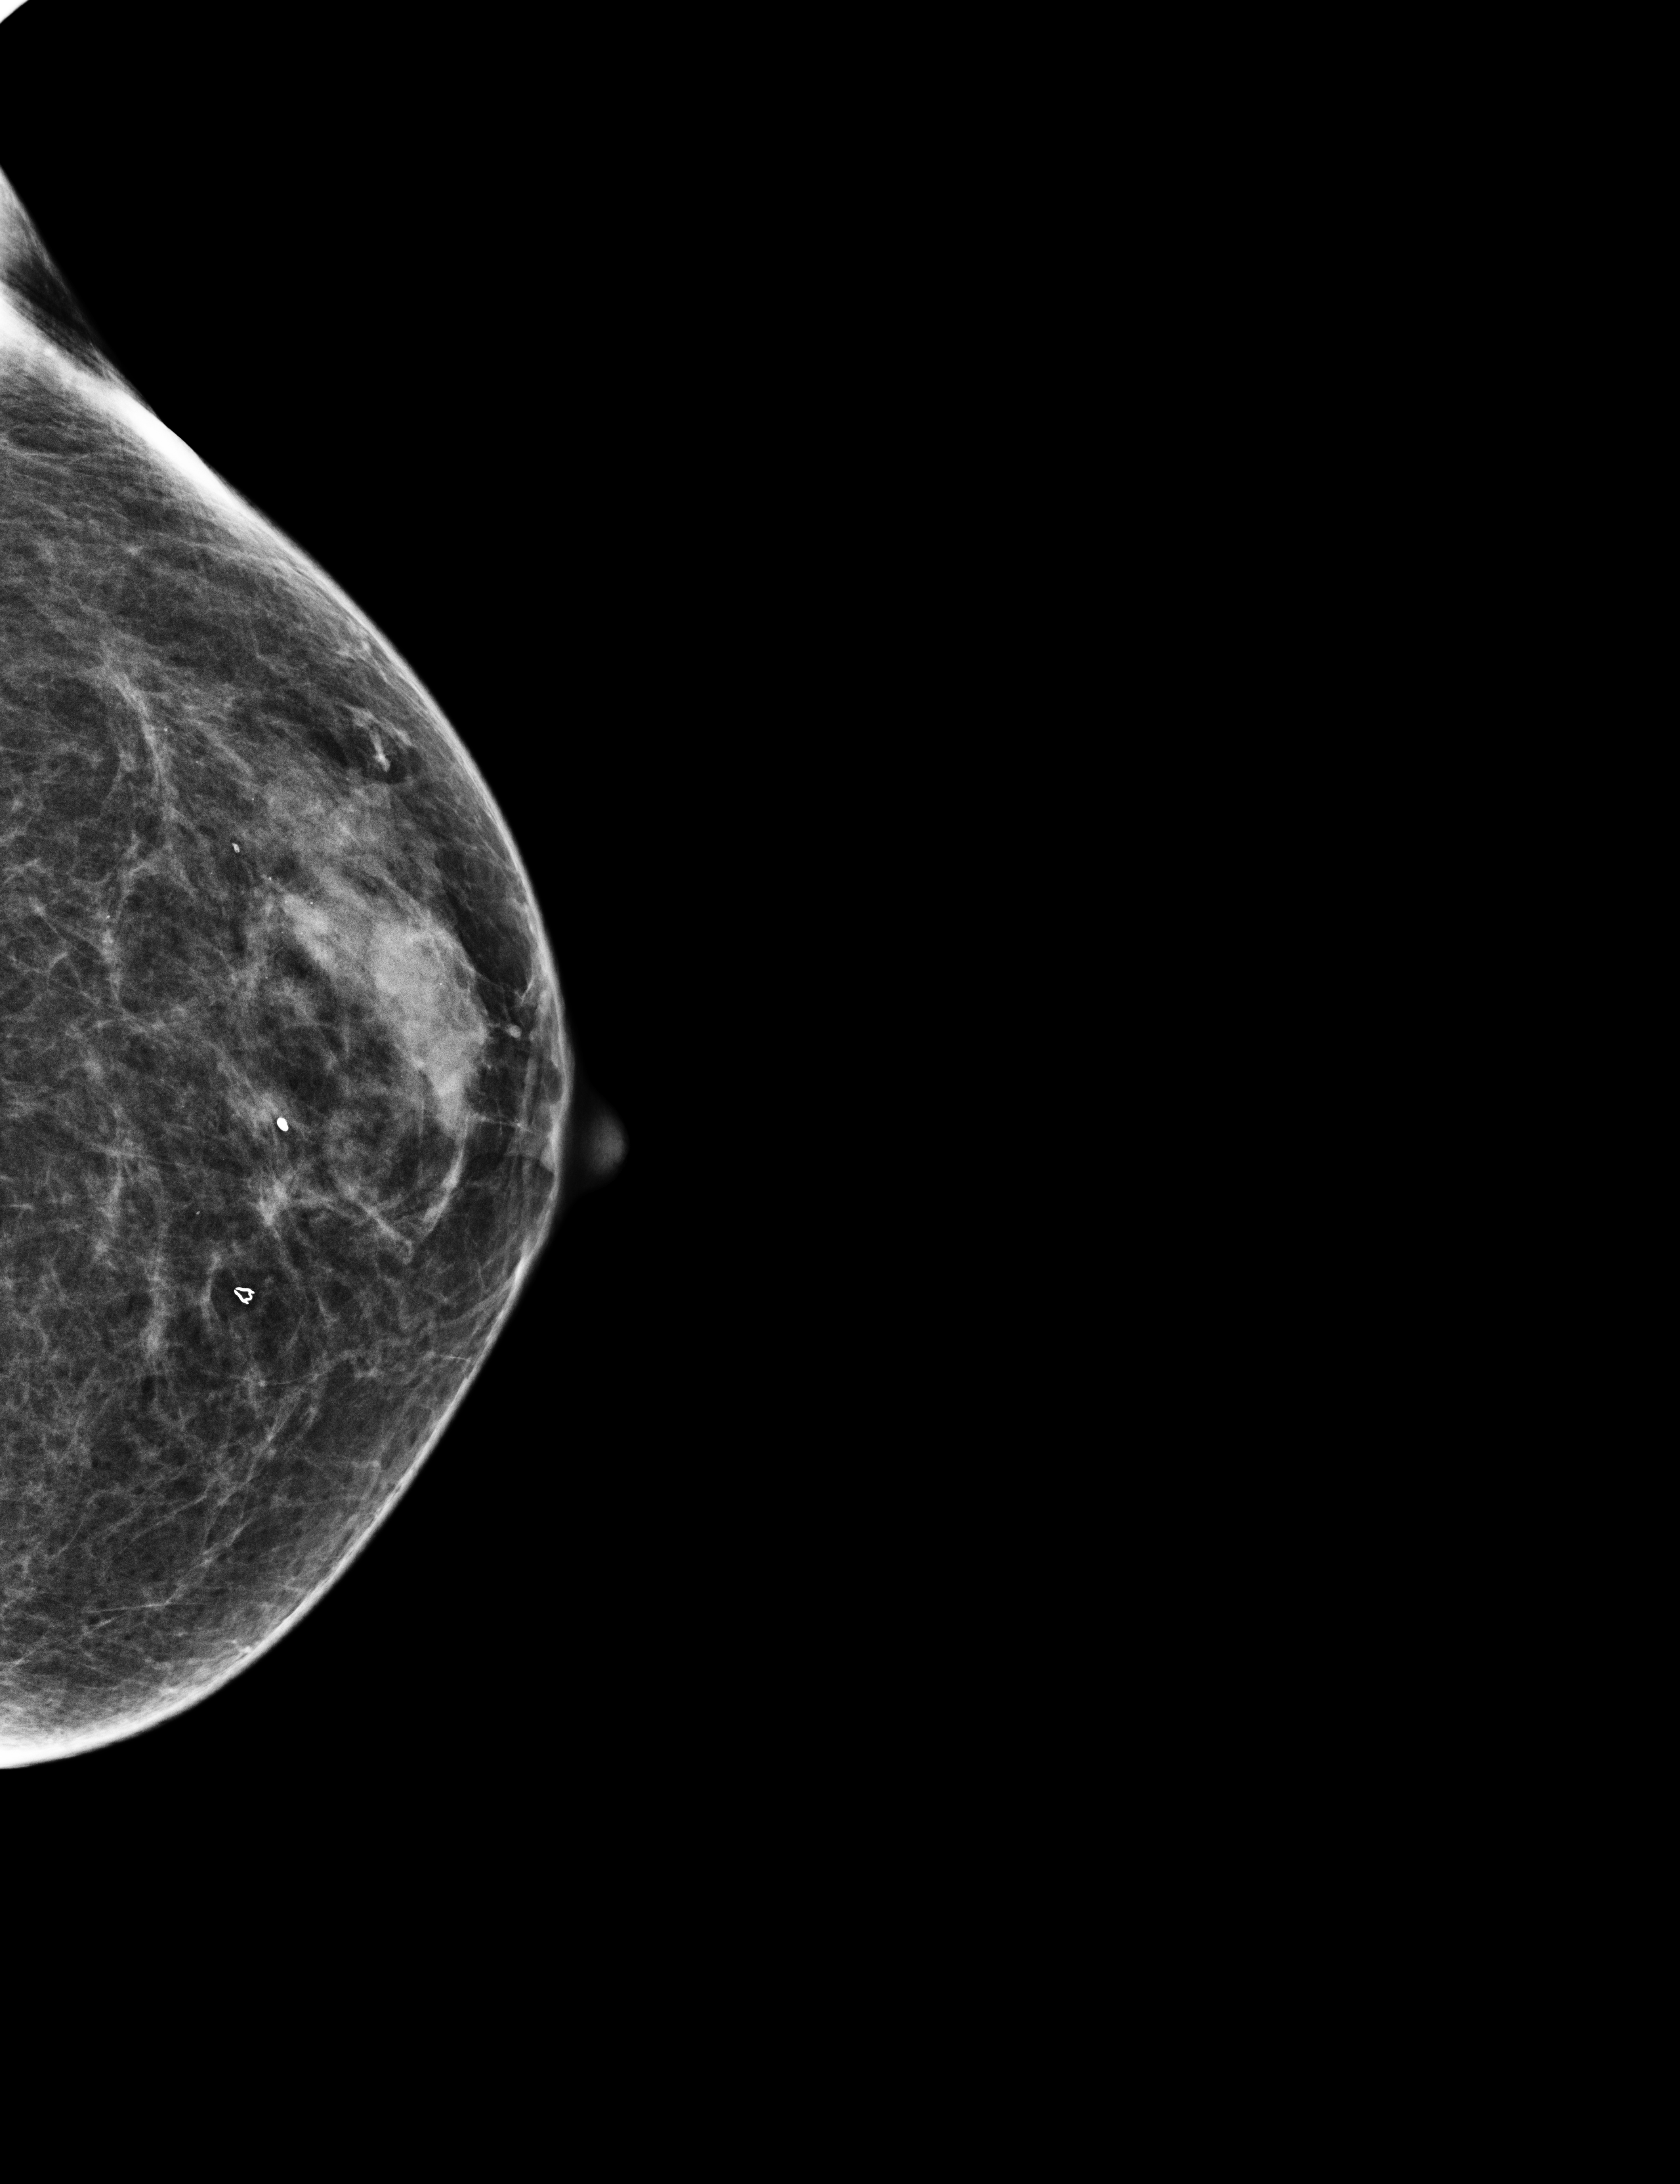
Annual screening mammography examination. Female patient, age 68 years.
Image type: full-field digital mammogram. Breast: left. Projection: craniocaudal (CC) view.